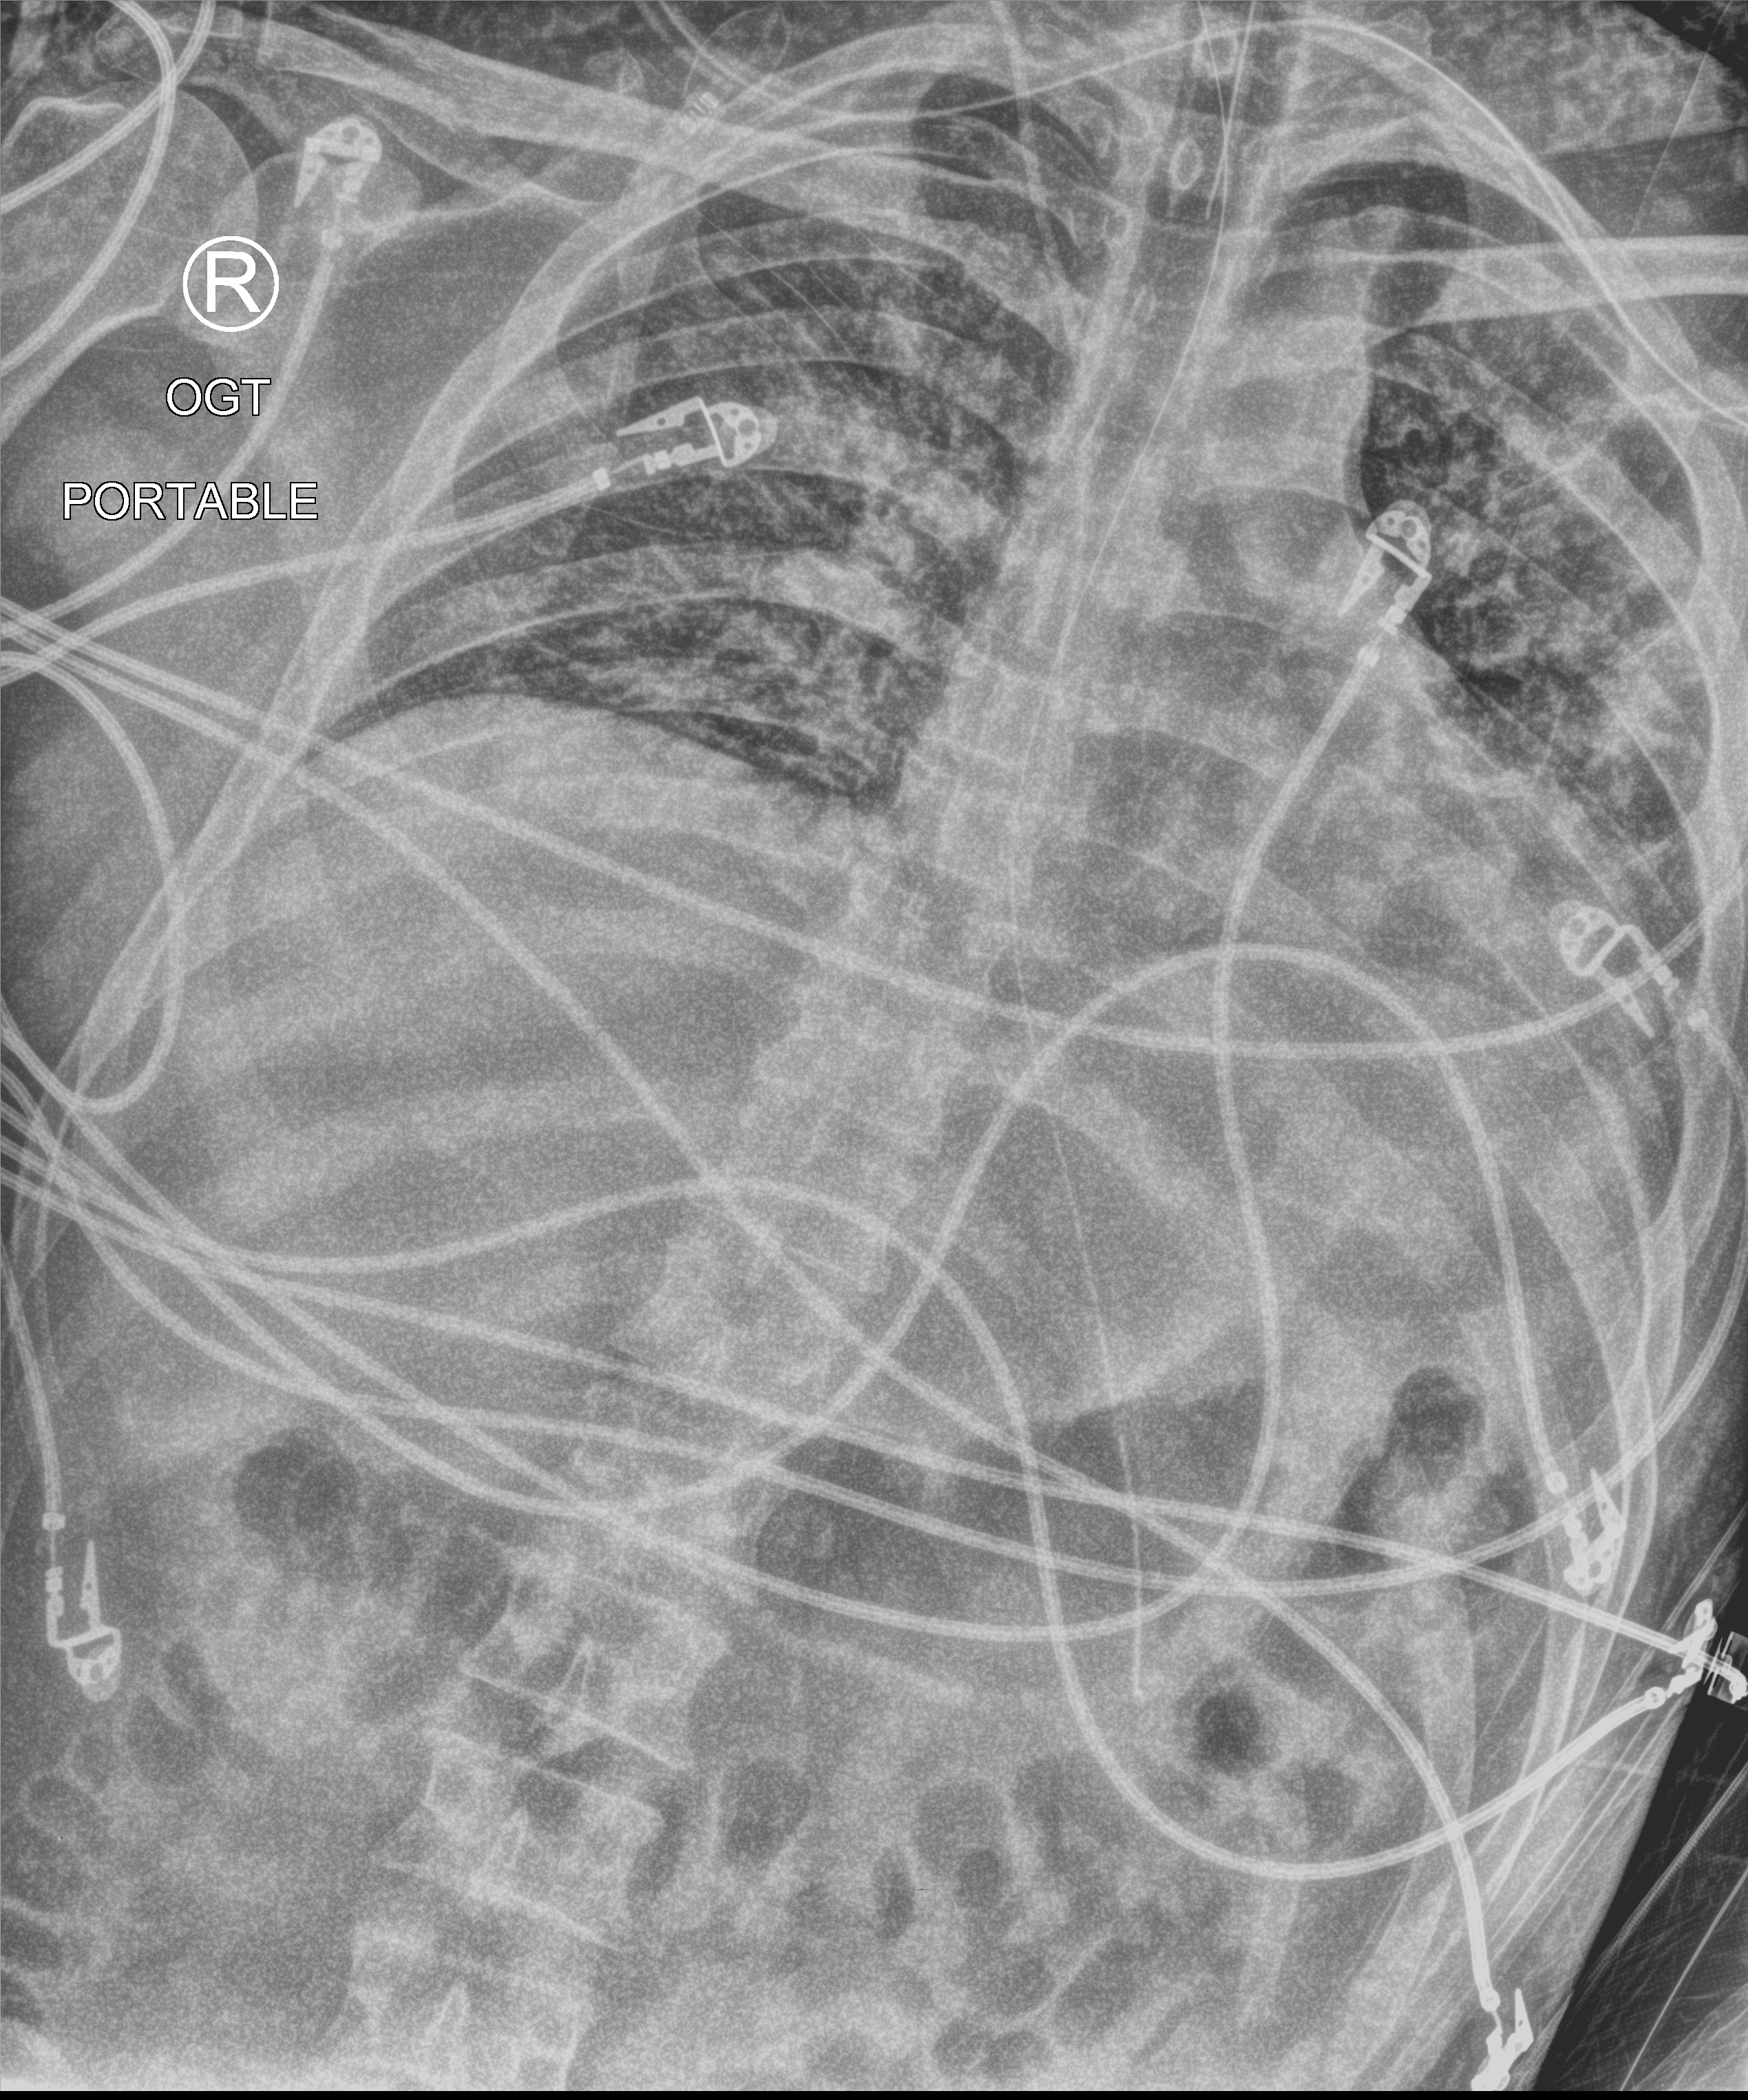
Portable chest radiograph, anteroposterior (AP) projection. Patient hospitalised with COVID-19; male, aged 18–59 years.
From the hospital-stay record, not from the radiograph (when in the stay this image was taken is not recorded):
- length of hospital stay: 20 days
- mechanically ventilated during this hospital stay: yes
- admitted to intensive care during this hospital stay: yes